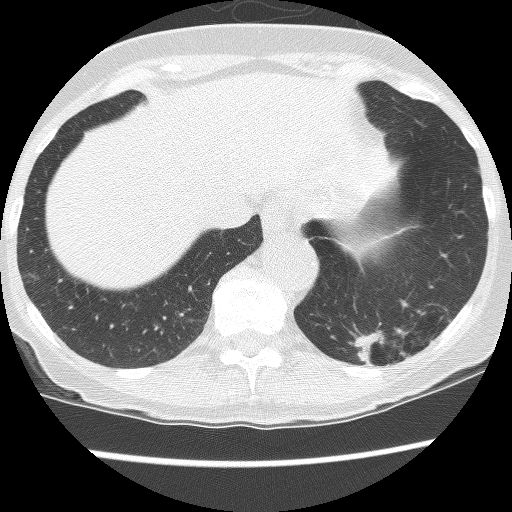
Axial slice from a low-dose chest CT screening exam; third screening round (two years after baseline); lung window (W 1500 / L -600 HU); lung (sharp) reconstruction kernel (BONE); 120 kVp; slice 102 of 130 in the series. Female, age 61 years at enrolment. Current smoker at enrolment.
Lesion marked by an expert reader, bounding box <335,295,440,386> (left, top, right, bottom; pixels). The screening reader recorded 2 non-calcified nodules or masses ≥4 mm on this exam (left lower lobe, left lower lobe); which of them this box marks is not recorded. Official screen result: positive, no significant change: stable abnormalities potentially related to lung cancer, unchanged since the prior screening exam.